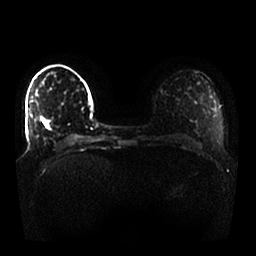
Breast MRI, one axial slice; slice 14 of 25 in the series (ordered by position); diffusion-weighted series; image 2 of 4 stored at this slice position (different b-values; order by instance number); 1.5 T; 4 mm slice thickness; 256 × 256 image matrix. Female patient.
Structures marked on this image (expert manual segmentation):
- tumour on diffusion-weighted imaging: bounding box <40,119,42,121> (left, top, right, bottom; pixels)